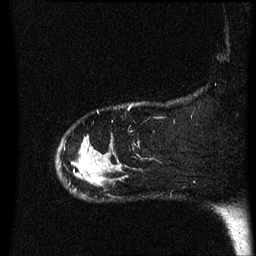
Breast MRI (dynamic contrast-enhanced), one sagittal slice; slice 56 of 60 in the series (ordered by position); dynamic contrast-enhanced series, image 2 of 3 at this slice position (ordered by acquisition); 1.5 T; TE 4.2 ms, TR 8.4 ms; 2.2 mm slice thickness; 256 × 256 image matrix, field of view 200 × 200 mm. Patient: female, 47 years.
Annotated regions visible in this slice (semi-automatic segmentation, software-assisted and operator-edited):
- analysis volume of interest (the breast-tissue region the enhancement analysis was run in; not a lesion): bounding box [x1, y1, x2, y2] px = [58, 137, 121, 197]
- tumour enhancement mask (voxels above the 70 % enhancement threshold inside the analysis volume of interest): [92, 180, 101, 182]